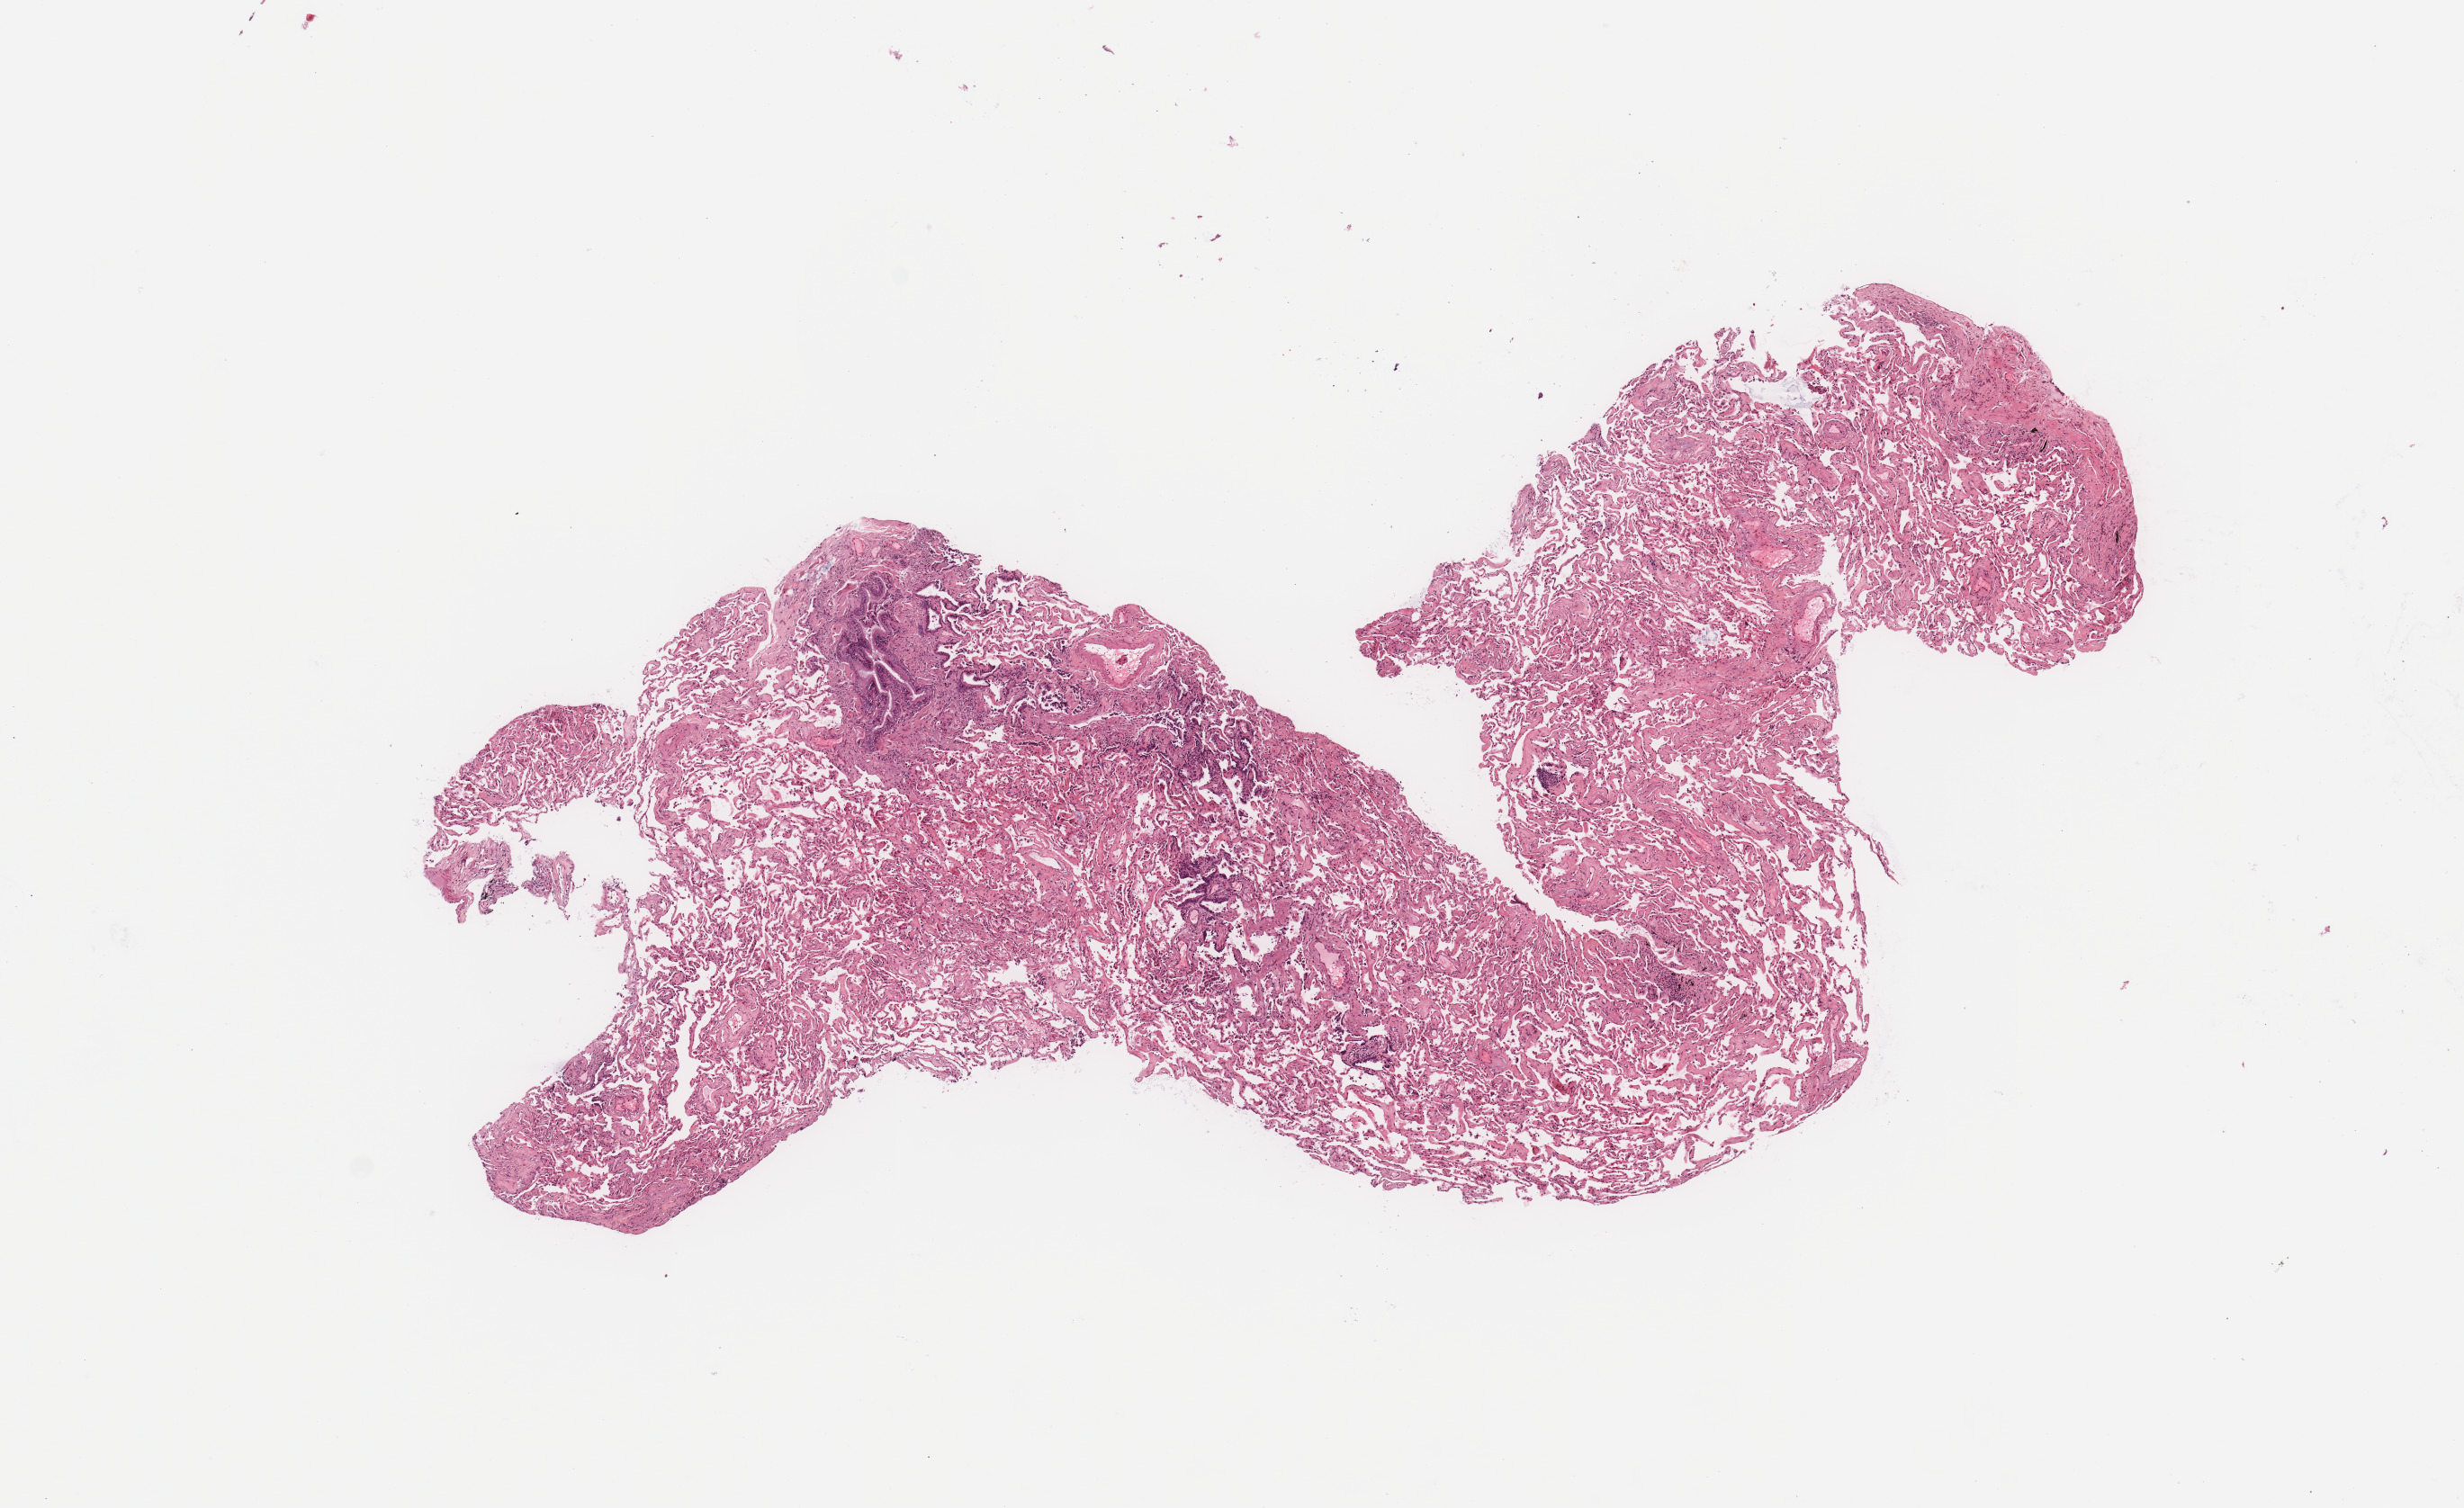
H&E-stained whole-slide image — low-resolution overview of the scanned area, about 10.8 x 6.6 mm (from a 20x scan); normal (non-tumour) tissue sample, lung. Female, 78 y/o.
* this section: normal (non-tumour) tissue from the same patient
* patient diagnosis: Adenocarcinoma, NOS